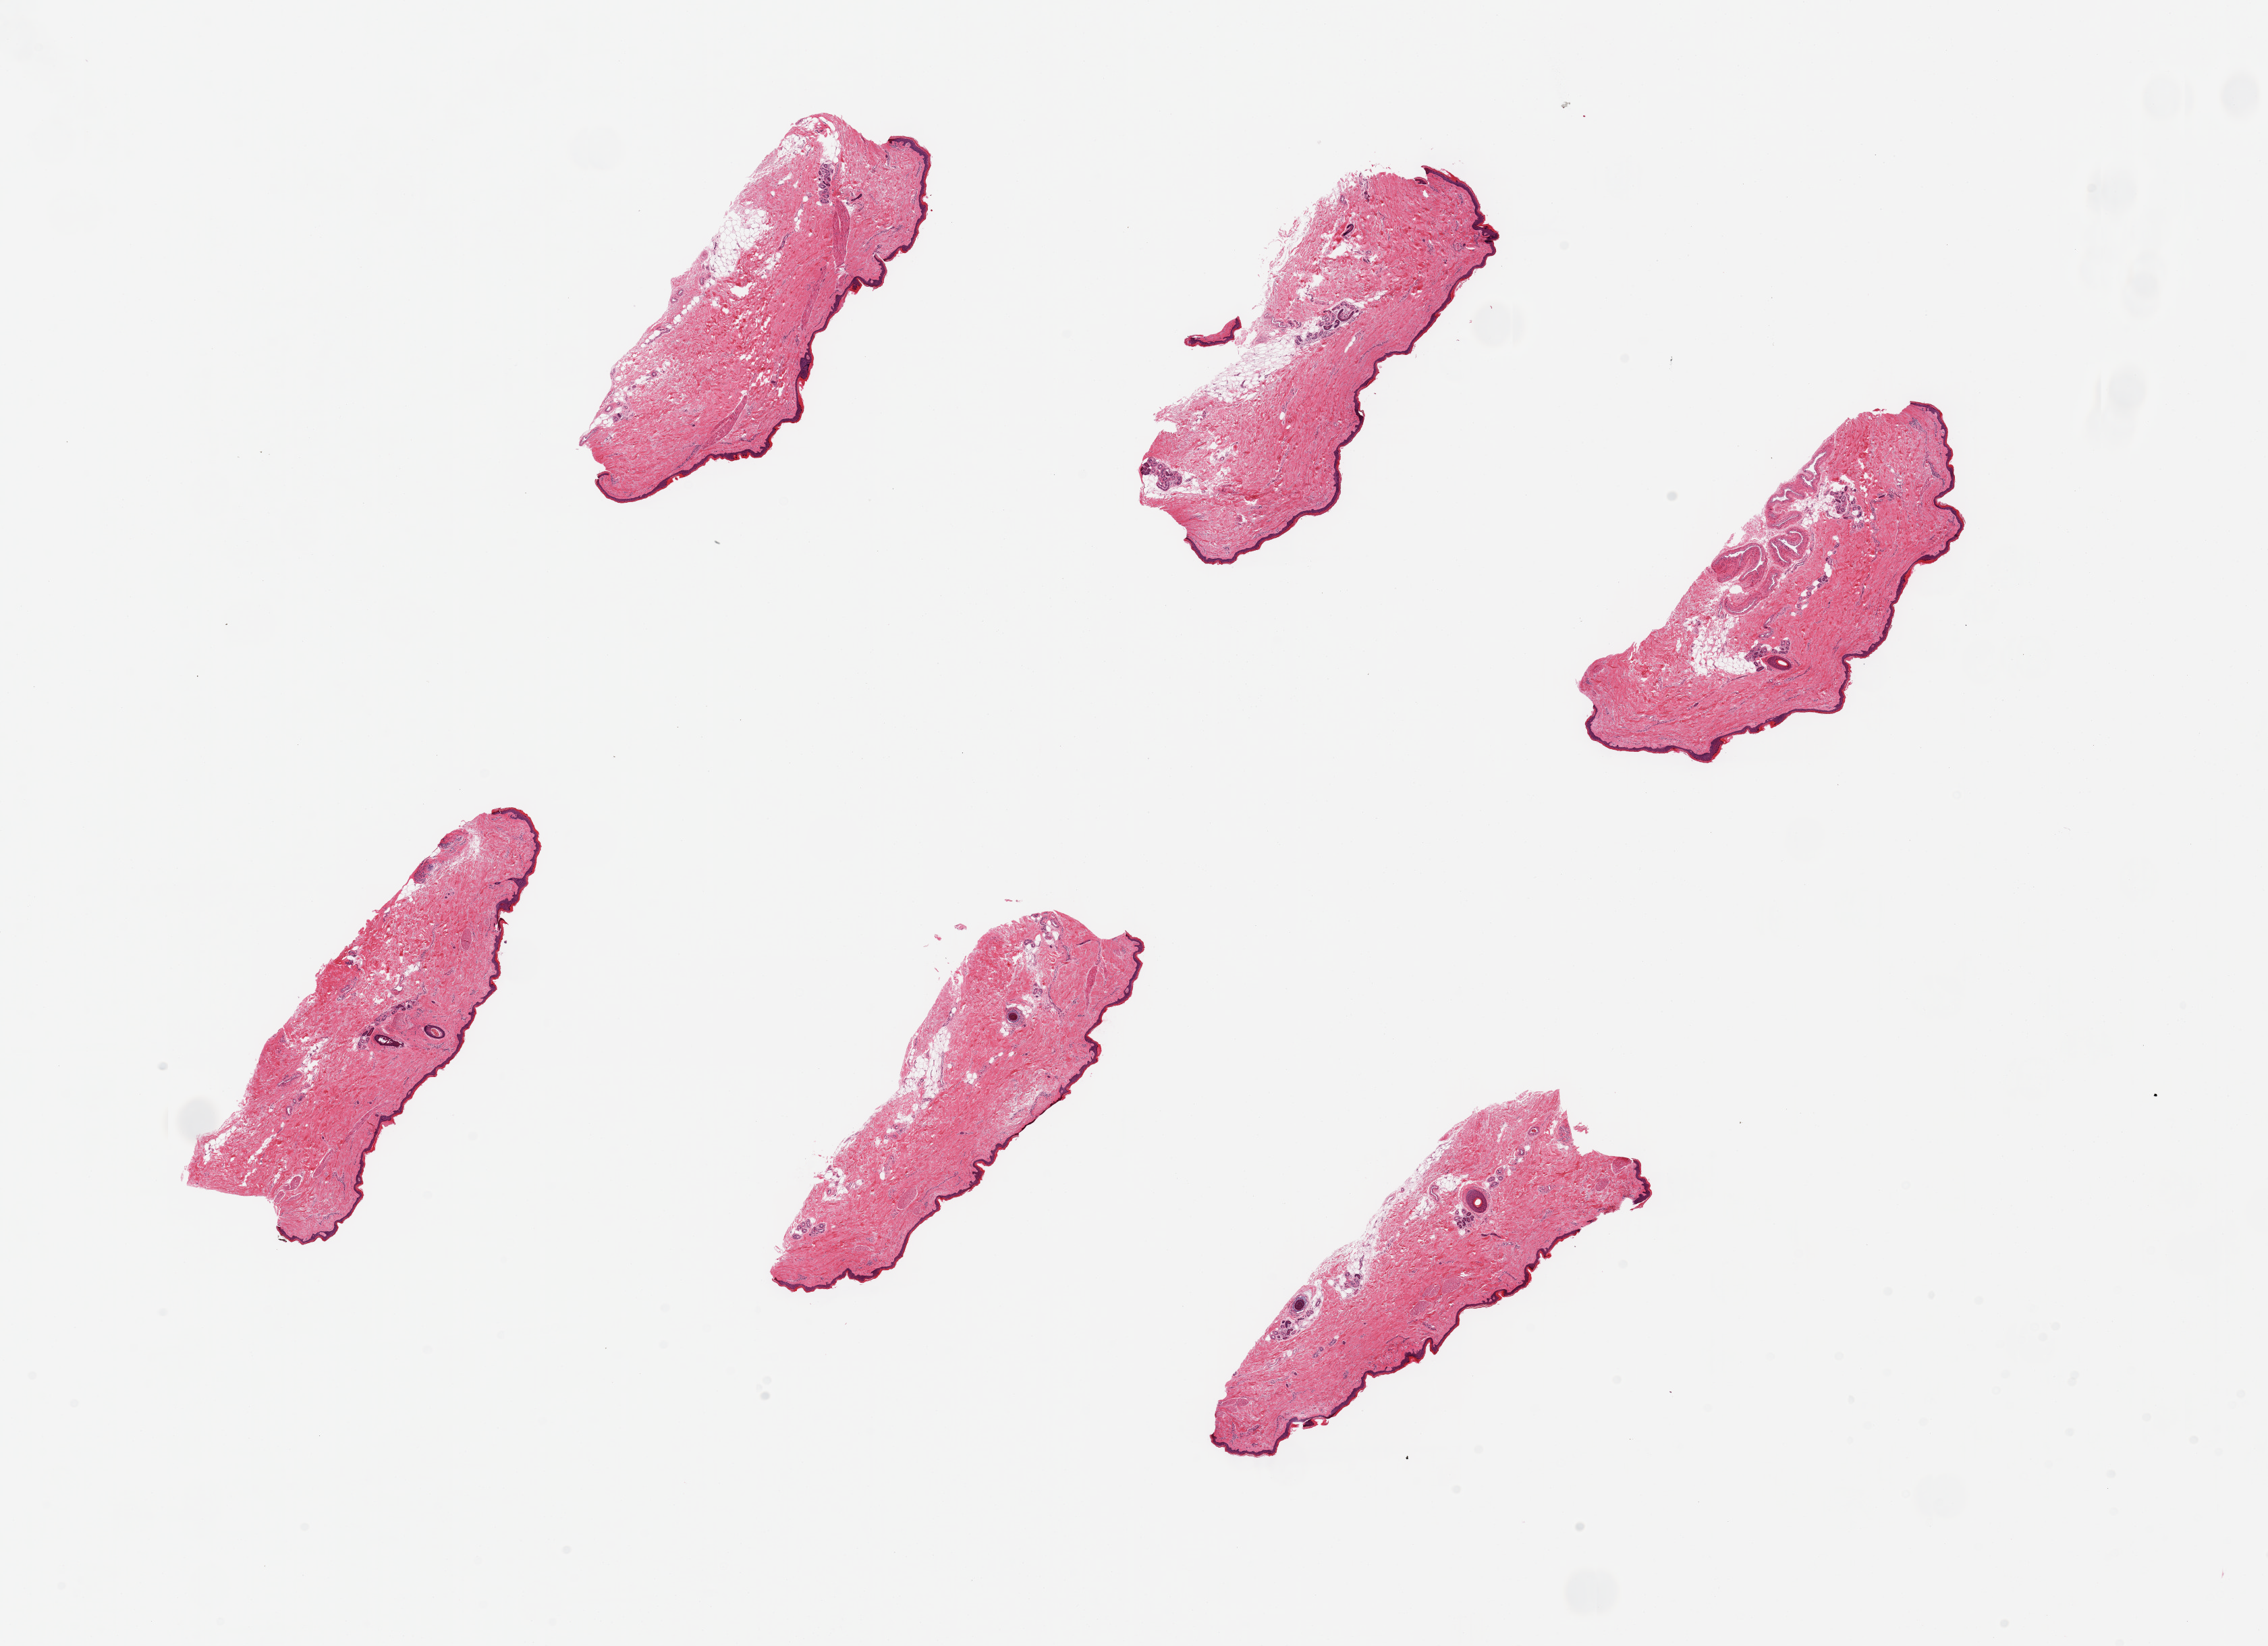
Whole-slide image, hematoxylin and eosin (H&E) stain, brightfield — whole scanned area (about 26.6 x 19.3 mm) shown as a low-resolution overview; PAXgene-fixed paraffin-embedded (PFPE) section; section of skin of lower leg (target tissue); donor tissue sample. Donor sex: male.
Reviewer comment on this tissue sample: 6 pieces, up to 6x2mm; subcutaneous fat well trimmed.